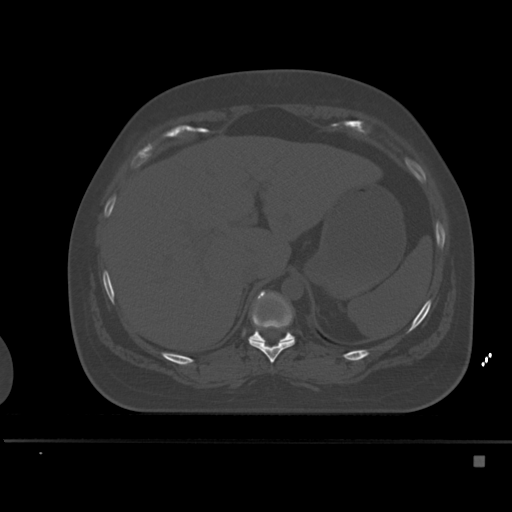
CT including the spine, one axial slice; slice 242 of 495 in the series (ordered by position); bone window (W 1800 / L 400 HU); 1.5 mm slice thickness; 512 × 512 image matrix. Patient: female, 33 years. From the clinical record (not read from this slice): primary cancer: breast; vertebrae with lytic lesions (as recorded): T1.
Outlined on this slice (semi-automatic segmentation, software-assisted and operator-edited):
- T10 vertebra: bounding box (x1, y1, x2, y2) in pixels: (248, 293, 296, 363)
- T11 vertebra: (249, 329, 294, 342)